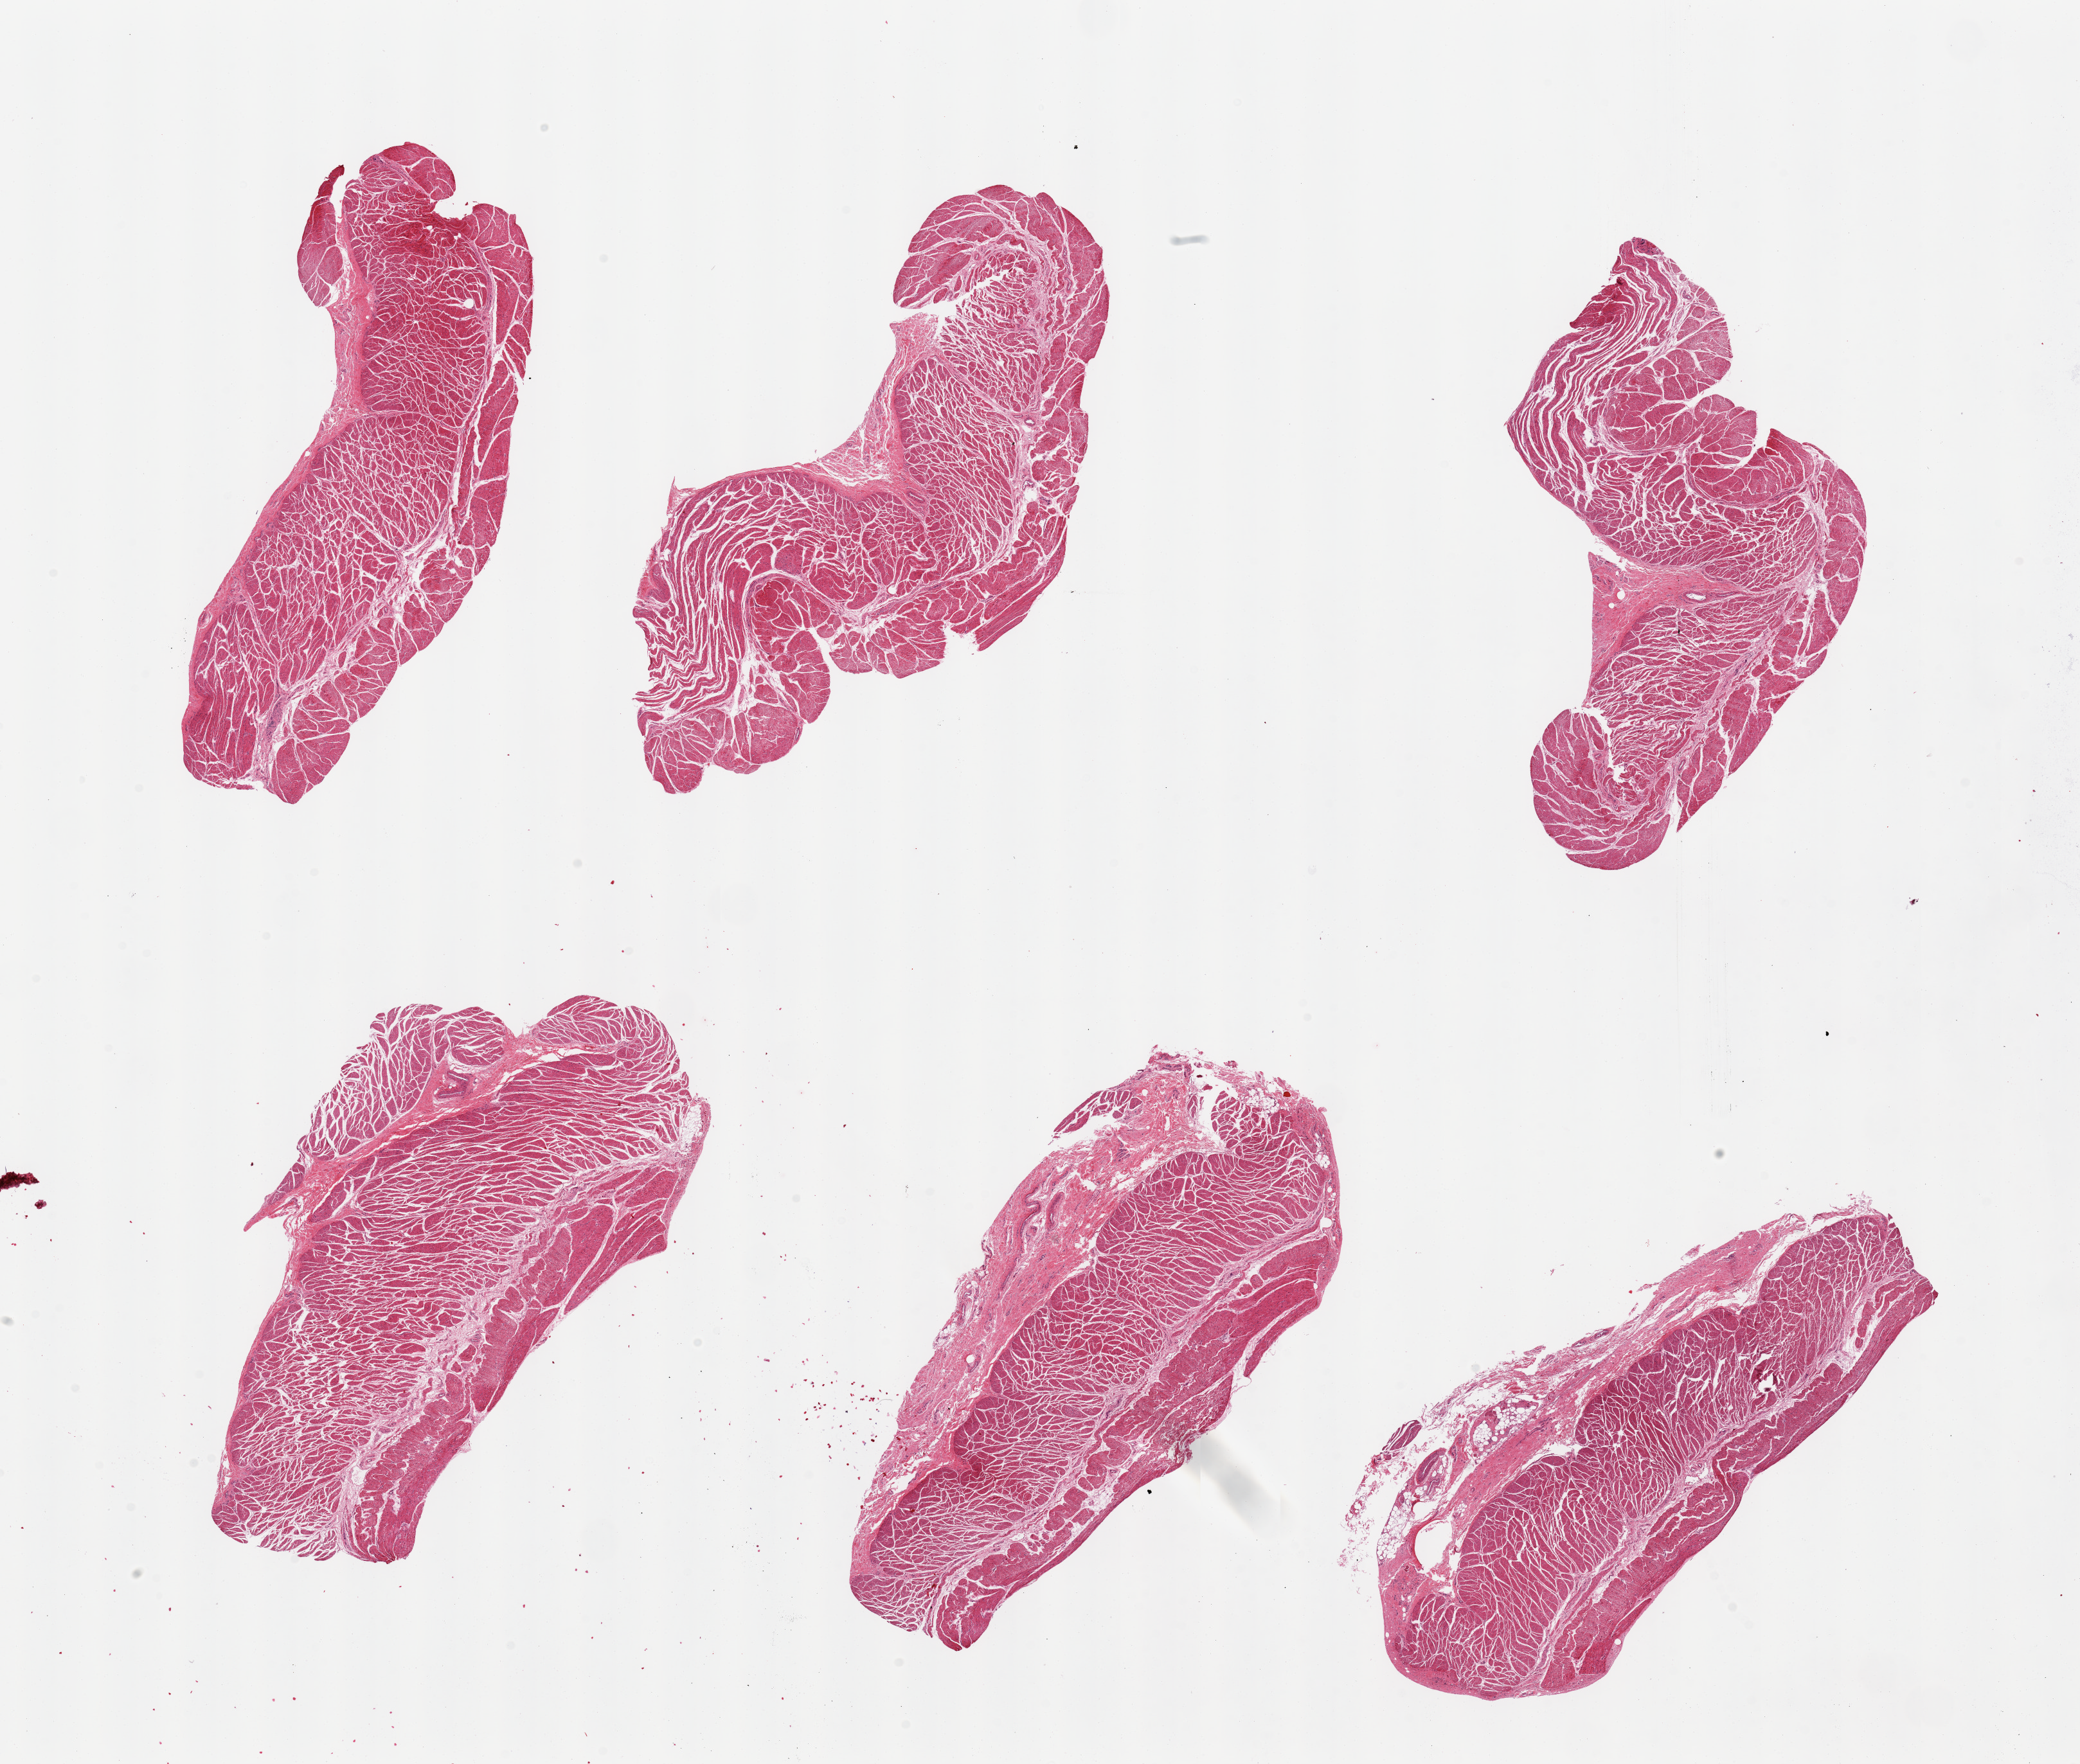
Digitized H&E-stained section — a low-resolution overview of the entire scanned area, about 25.6 x 21.7 mm (from a 20x scan), PAXgene-fixed, paraffin-embedded tissue, sampled site (target tissue): esophageal muscle, tissue donor sample. Male donor.
* reviewer comment on this tissue sample: 6 pieces, all muscularis, good specimens